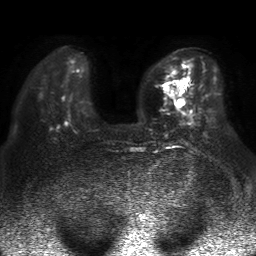
Breast MRI, one axial slice. Position 13 of 50 along the scan axis. Diffusion-weighted series; image 2 of 4 stored at this slice position (different b-values; order by instance number). 1.5 T. 4 mm slice thickness. 256 × 256 image matrix. Female patient.
Annotated regions visible in this slice (manually delineated by an expert):
- tumour on diffusion-weighted imaging: bounding box [x1, y1, x2, y2] px = [179, 99, 184, 105]